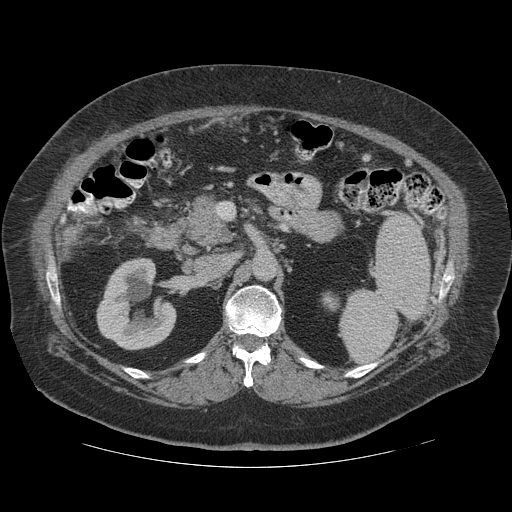
Contrast-enhanced abdominal CT (liver protocol), one axial slice; slice 53 of 121 in the series (ordered by position); 140 kVp; soft-tissue window (W 400 / L 40 HU); 512 × 512 image matrix, field of view 420 × 420 mm. Case-level facts recorded for this patient, not image findings: diagnosis: hepatocellular carcinoma (patient treated with transarterial chemoembolisation; whether this scan precedes or follows treatment is not stated here); TNM stage (as recorded): Stage-IIIA; Child-Pugh class: A; tumour differentiation: well differentiated.
Annotated regions visible in this slice (semi-automatic segmentation, software-assisted and operator-edited):
- liver parenchyma outside the tumour (the mass and vessels are separate outlines, so this box may not span the whole liver): box from (x=62, y=235) to (x=72, y=255) px